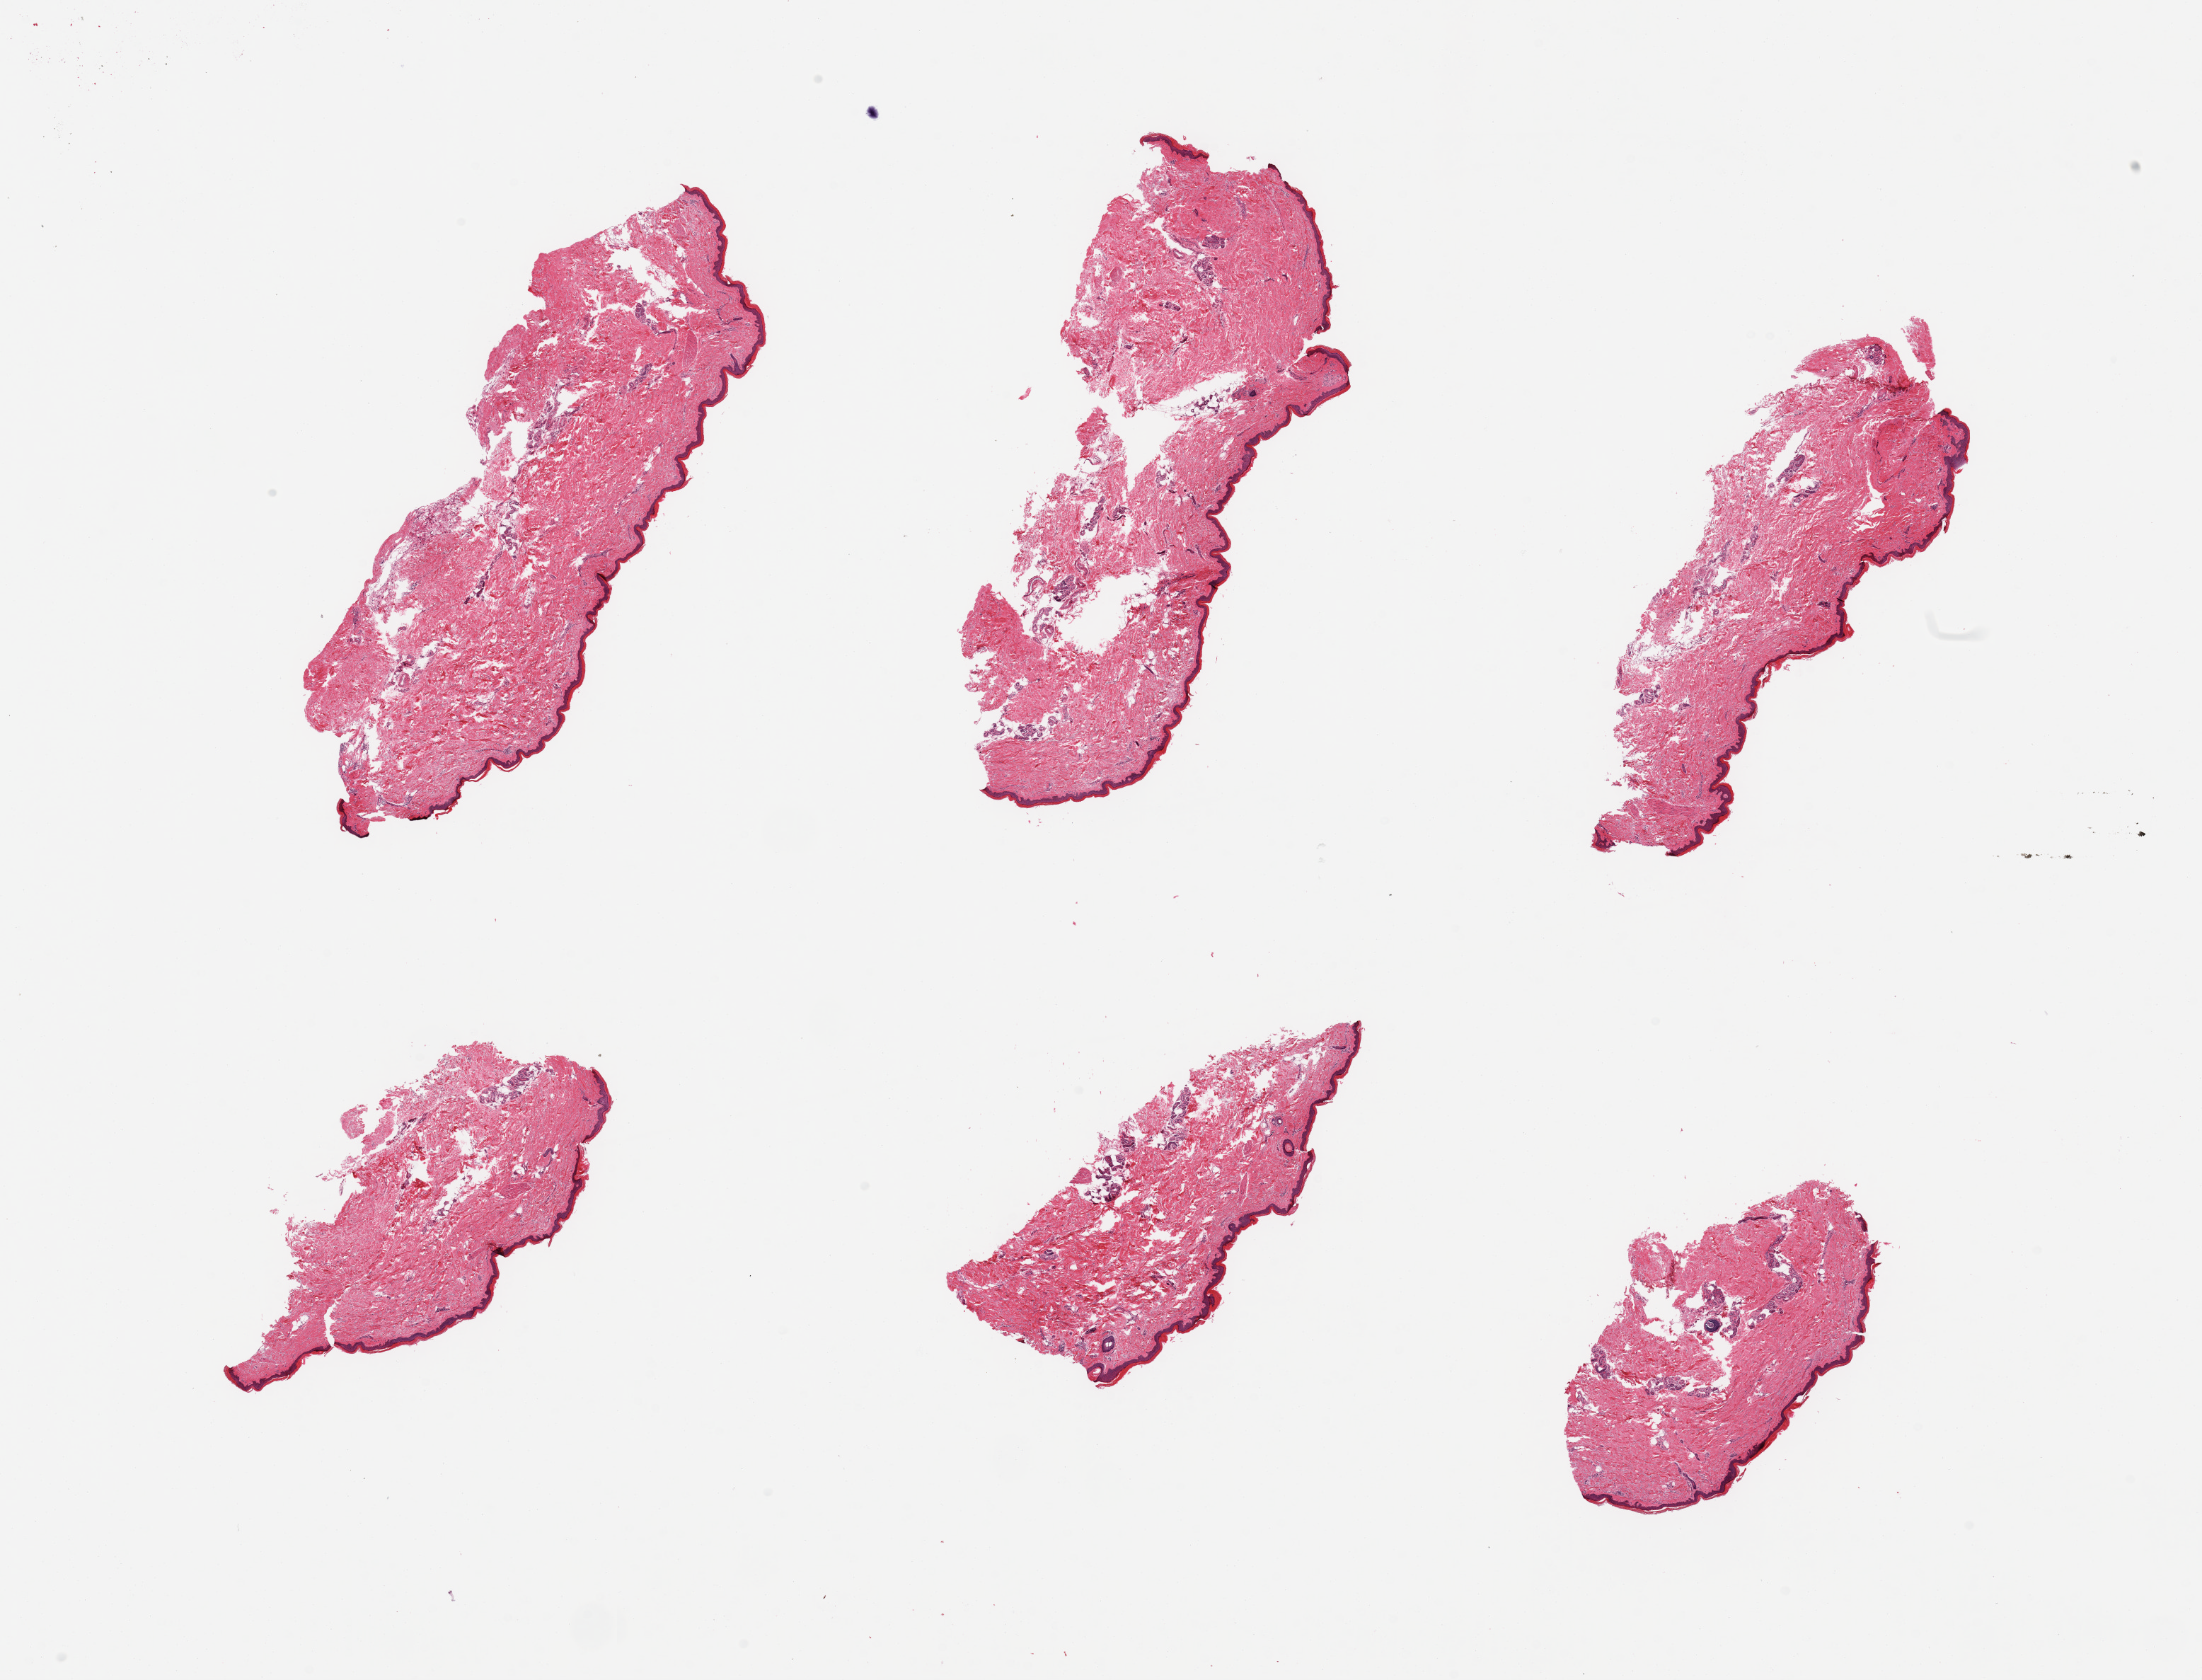
Whole-slide image, H&E stain, a low-resolution overview of the entire scanned area, about 24.6 x 18.8 mm (acquisition: 20x scan), PAXgene-fixed paraffin-embedded (PFPE) section, sampled site (target tissue): skin of lower leg, tissue donor sample.
Reviewer comment on this tissue sample: 6 pieces; well trimmed; 5% dermal fat.